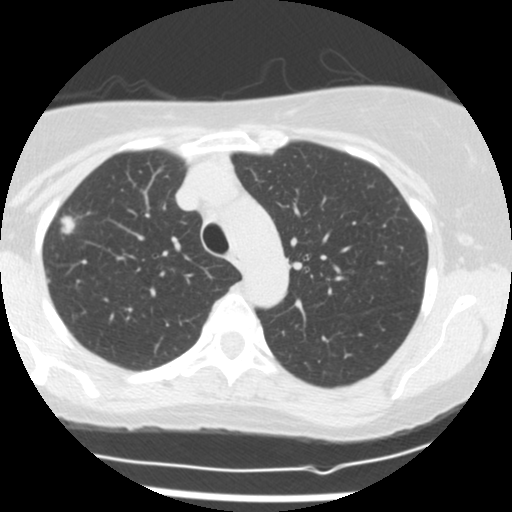
Chest CT (low-dose screening protocol), one axial image. Baseline screening round. Lung window (W 1500 / L -600 HU). 2.5 mm slice thickness. Slice 44 of 160 in the series. 512 × 512 image matrix, field of view 300 × 300 mm. Female participant, aged 58 years at enrolment. Former smoker at enrolment.
Lesion marked by an expert reader, box from (x=43, y=203) to (x=92, y=240) px. The exam's reader record, not a measurement of the box and not confirmed to be the same lesion: non-calcified nodule or mass ≥4 mm, right upper lobe, 12 × 9 mm, spiculated (stellate) margins, soft tissue attenuation.